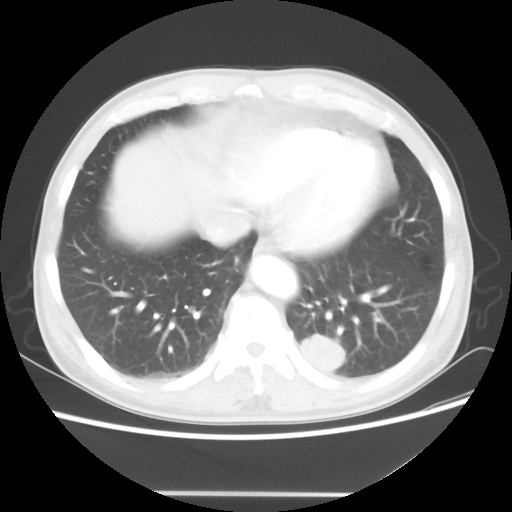
Chest CT, one axial slice. Reconstruction kernel STANDARD. 100 kVp. Lung window (W 1500 / L -600 HU). 5 mm slice thickness. 512 × 512 image matrix, field of view 360 × 360 mm. Male patient, age 55 years. From the clinical record (not read from this slice): clinical TNM (as recorded): T1c N3 M0.
Annotated regions visible in this slice (bounding box drawn by a radiologist):
- lung tumour (recorded histology: small cell carcinoma): bounding box [x1, y1, x2, y2] px = [294, 329, 347, 378]